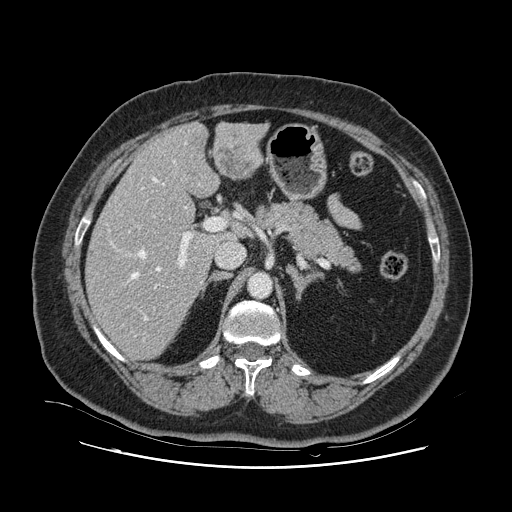
Contrast-enhanced abdominal CT, one axial slice. 120 kVp. Intravenous contrast given. Soft-tissue window (W 400 / L 40 HU). 512 × 512 image matrix, field of view 391 × 391 mm. Female patient, age 73 years. Case-level facts recorded for this patient, not image findings: diagnosis: colorectal cancer liver metastases, imaged before liver resection; multiple liver metastases: no; largest metastasis: 7 cm; disease in both lobes: no.
Outlined on this slice (expert manual segmentation):
- hepatic veins: bounding box [x1, y1, x2, y2] px = [109, 160, 200, 342]
- liver: [87, 124, 263, 359]
- planned liver remnant (the part of the liver to remain after resection): [87, 150, 218, 359]
- portal vein (with intrahepatic branches): [129, 218, 225, 309]
- liver metastasis: [218, 150, 254, 176]